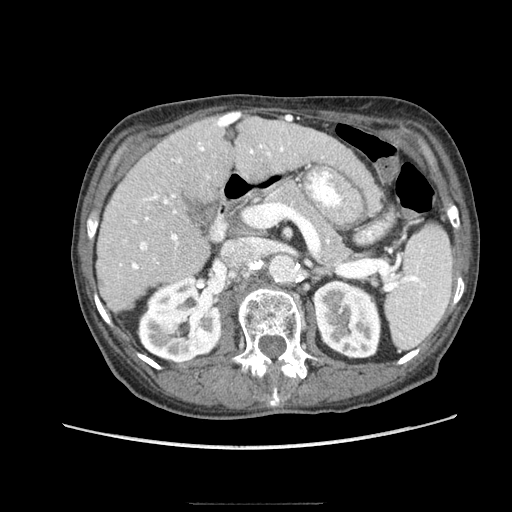
Contrast-enhanced abdominal CT (liver protocol), one axial slice; position 42 of 83 along the scan axis; reconstruction kernel STANDARD; 140 kVp; soft-tissue window (W 400 / L 40 HU); 2.5 mm slice thickness; 512 × 512 image matrix. Case-level facts recorded for this patient, not image findings: diagnosis: hepatocellular carcinoma (patient treated with transarterial chemoembolisation; whether this scan precedes or follows treatment is not stated here); TNM stage (as recorded): Stage-I; Child-Pugh class: A; tumour differentiation: moderately differentiated; tumour nodularity: uninodular.
Annotated regions visible in this slice (semi-automatic segmentation, software-assisted and operator-edited):
- liver parenchyma outside the tumour (the mass and vessels are separate outlines, so this box may not span the whole liver): bounding box (x1, y1, x2, y2) in pixels: (96, 114, 348, 312)
- liver vessels: (119, 114, 290, 270)